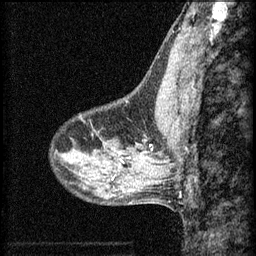
Breast MRI (dynamic contrast-enhanced), one sagittal slice; position 20 of 60 along the scan axis; 3 images stored at this slice position (order not interpretable as contrast timing); 1.5 T; TE 4.2 ms, TR 8.2 ms; 2 mm slice thickness; 256 × 256 image matrix, field of view 180 × 180 mm. Female patient, age 40 years.
Outlined on this slice (semi-automatically segmented with operator editing):
- analysis volume of interest (the breast-tissue region the enhancement analysis was run in; not a lesion): bounding box [x1, y1, x2, y2] px = [104, 116, 159, 165]
- tumour enhancement mask (voxels above the 70 % enhancement threshold inside the analysis volume of interest): [120, 158, 131, 163]